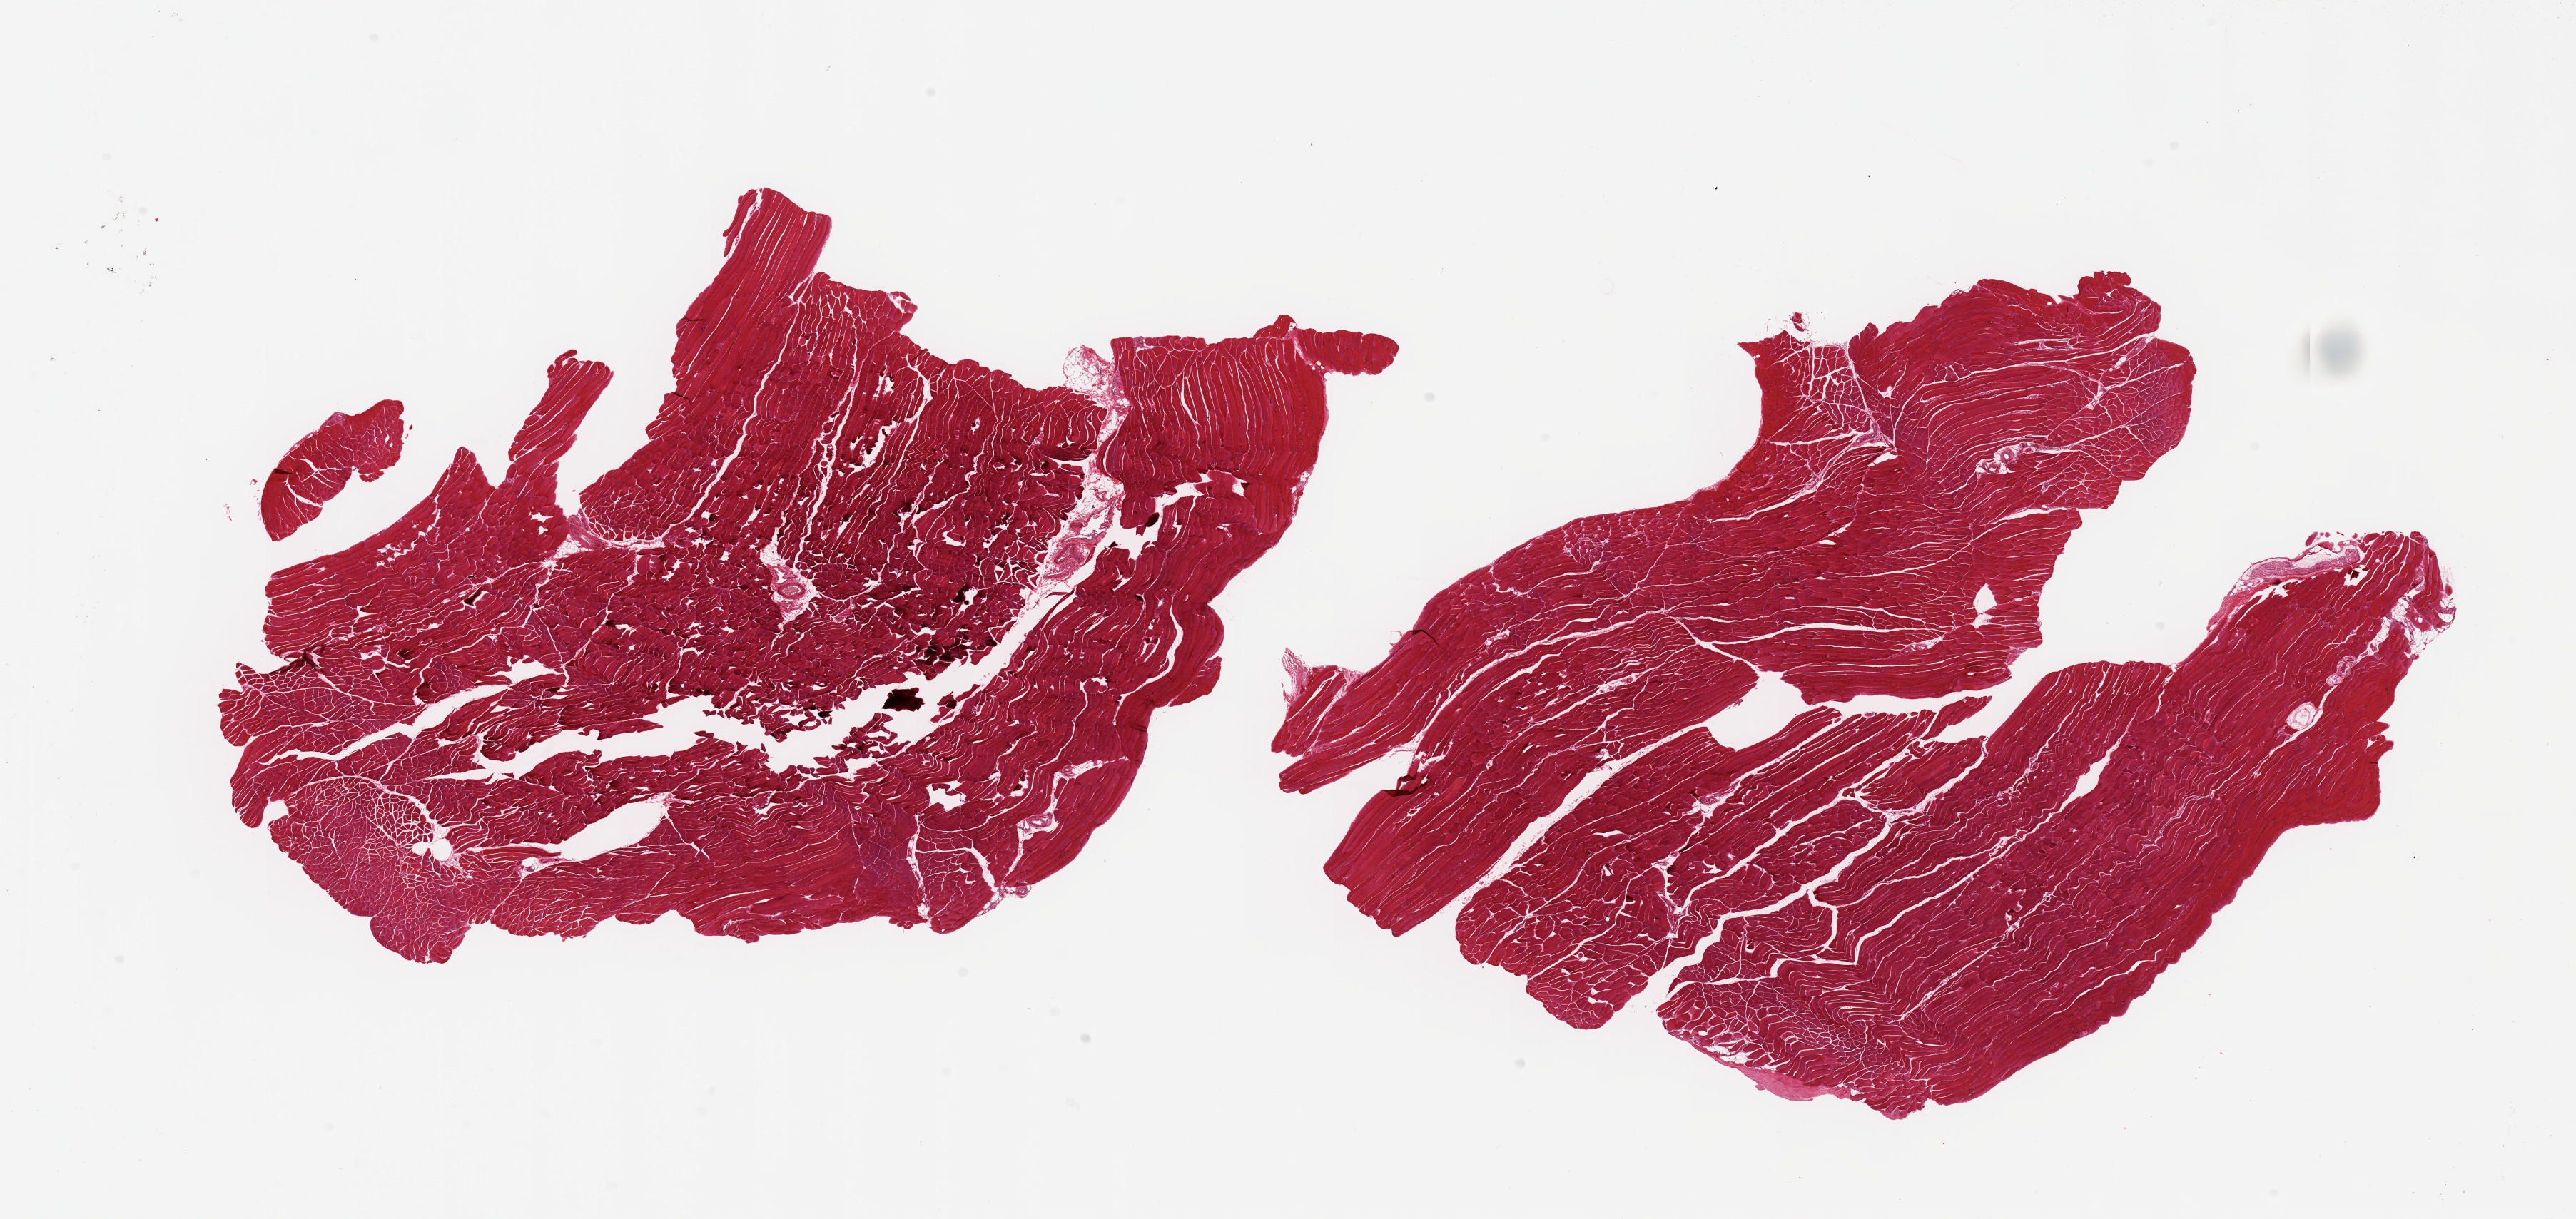
Digitized hematoxylin and eosin (H&E)-stained section — whole scanned area (about 28.5 x 13.5 mm) shown as a low-resolution overview, PAXgene-fixed, paraffin-embedded tissue, target tissue: skeletal muscle, tissue donor sample. Female donor.
Reviewer comment on this tissue sample: 2 pieces.